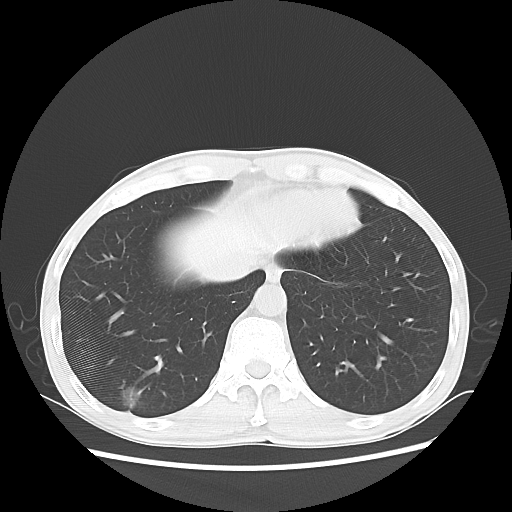
Chest CT, one axial slice; slice 17 of 68 in the series (ordered by position); lung window (W 1500 / L -600 HU); 5 mm slice thickness; 512 × 512 image matrix. Male patient, age 60 years. From the clinical record (not read from this slice): clinical TNM (as recorded): T1c N0 M0.
Structures marked on this image (bounding box drawn by a radiologist):
- lung tumour (recorded histology: adenocarcinoma): bounding box (x1, y1, x2, y2) in pixels: (115, 382, 148, 421)